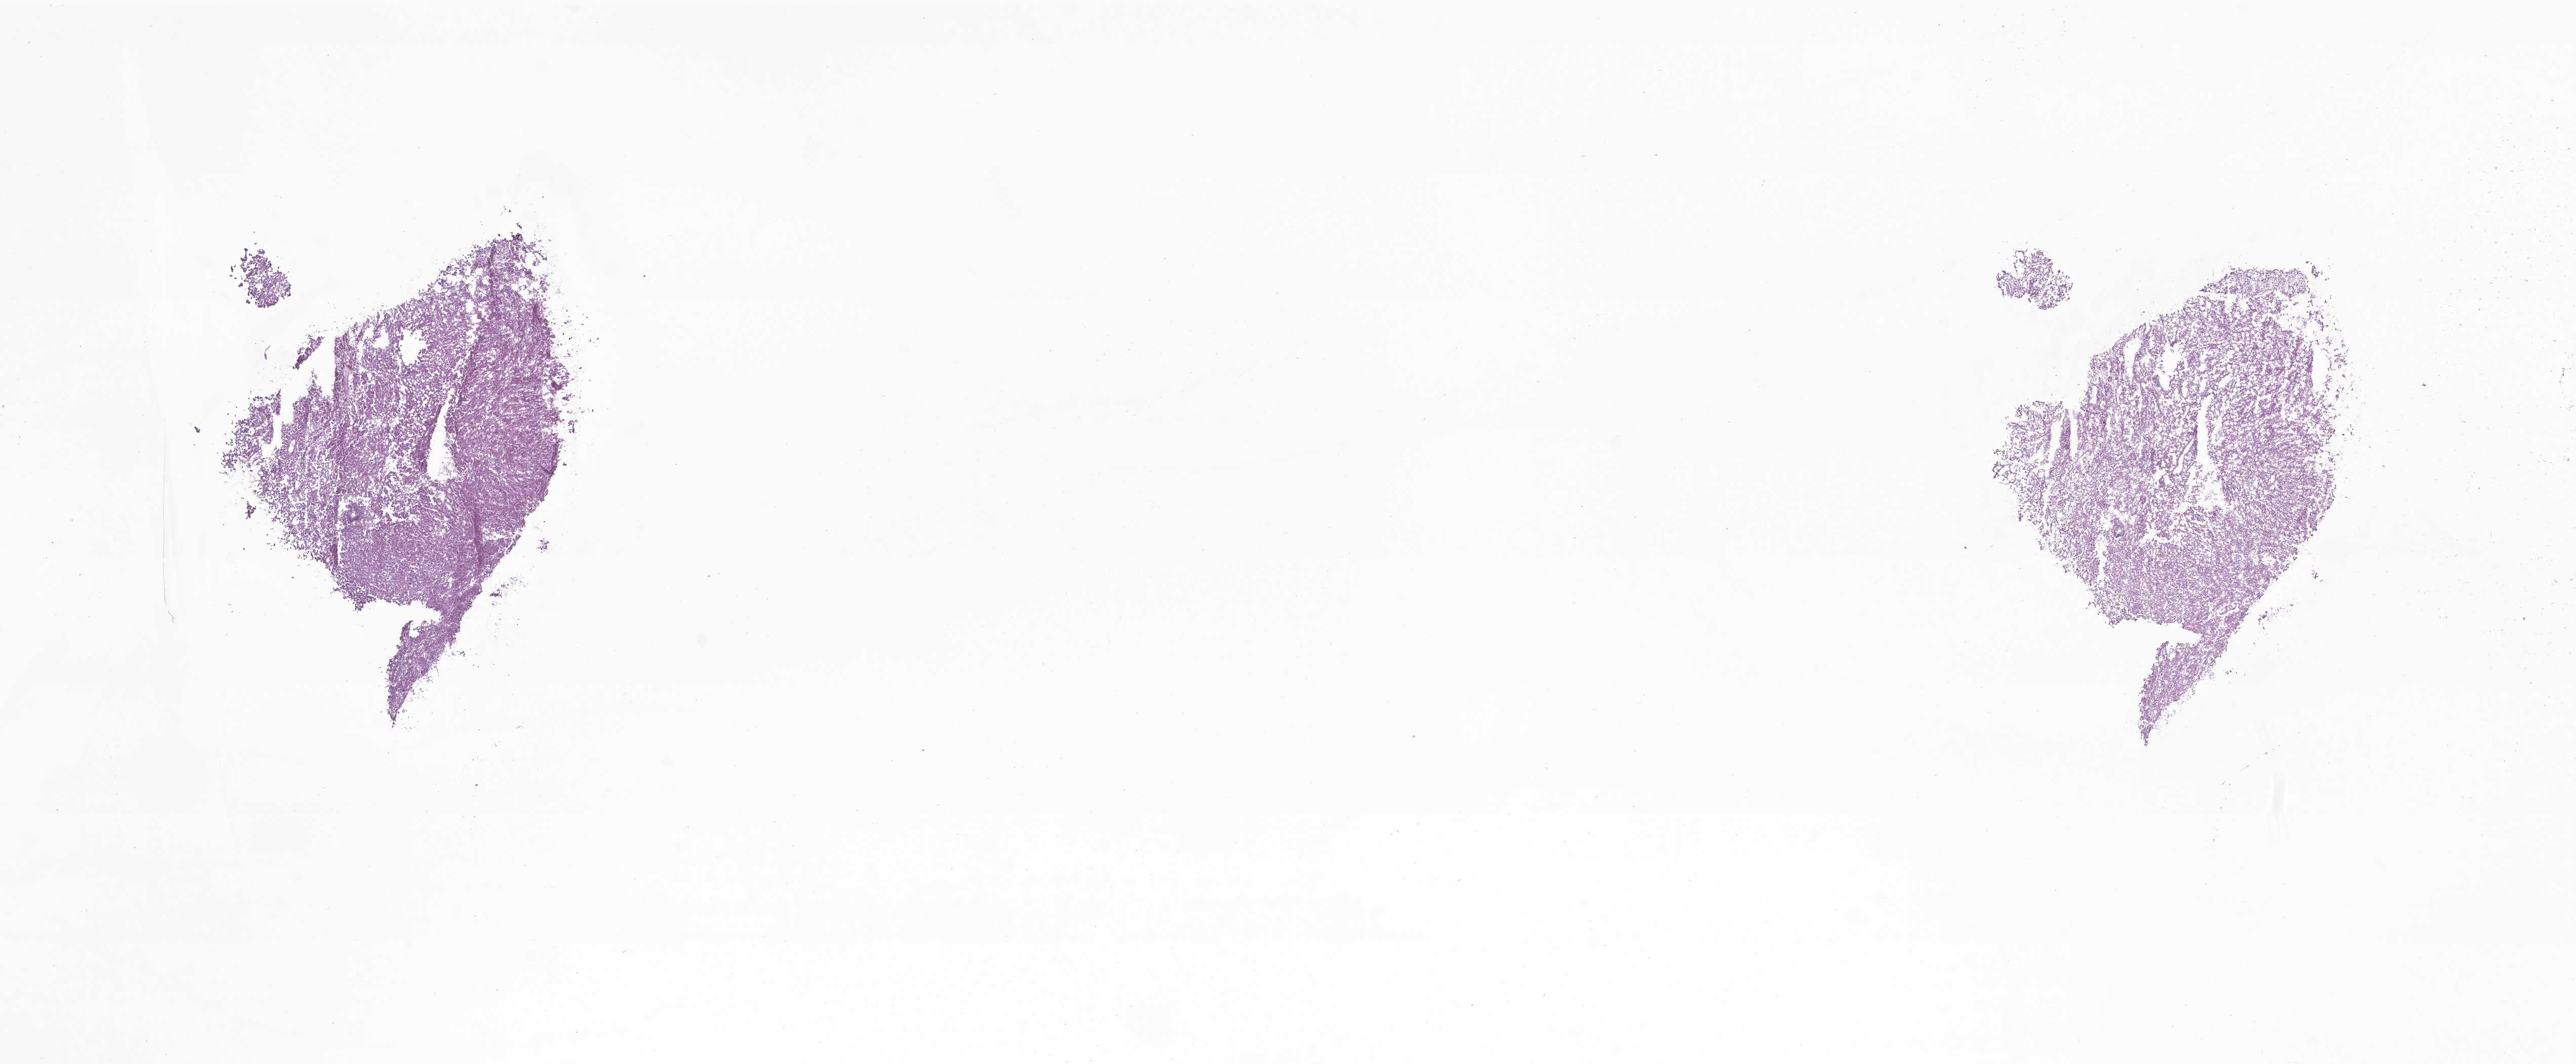
Hematoxylin and eosin (H&E) whole-slide image of tumor tissue from the temporal lobe, low-resolution overview of the scanned area, about 21.4 x 8.9 mm, cryosection (OCT / tissue freezing medium). Patient: male, age 124 months (10 years 4 months).
- diagnosis: Pleomorphic xanthoastrocytoma, NOS